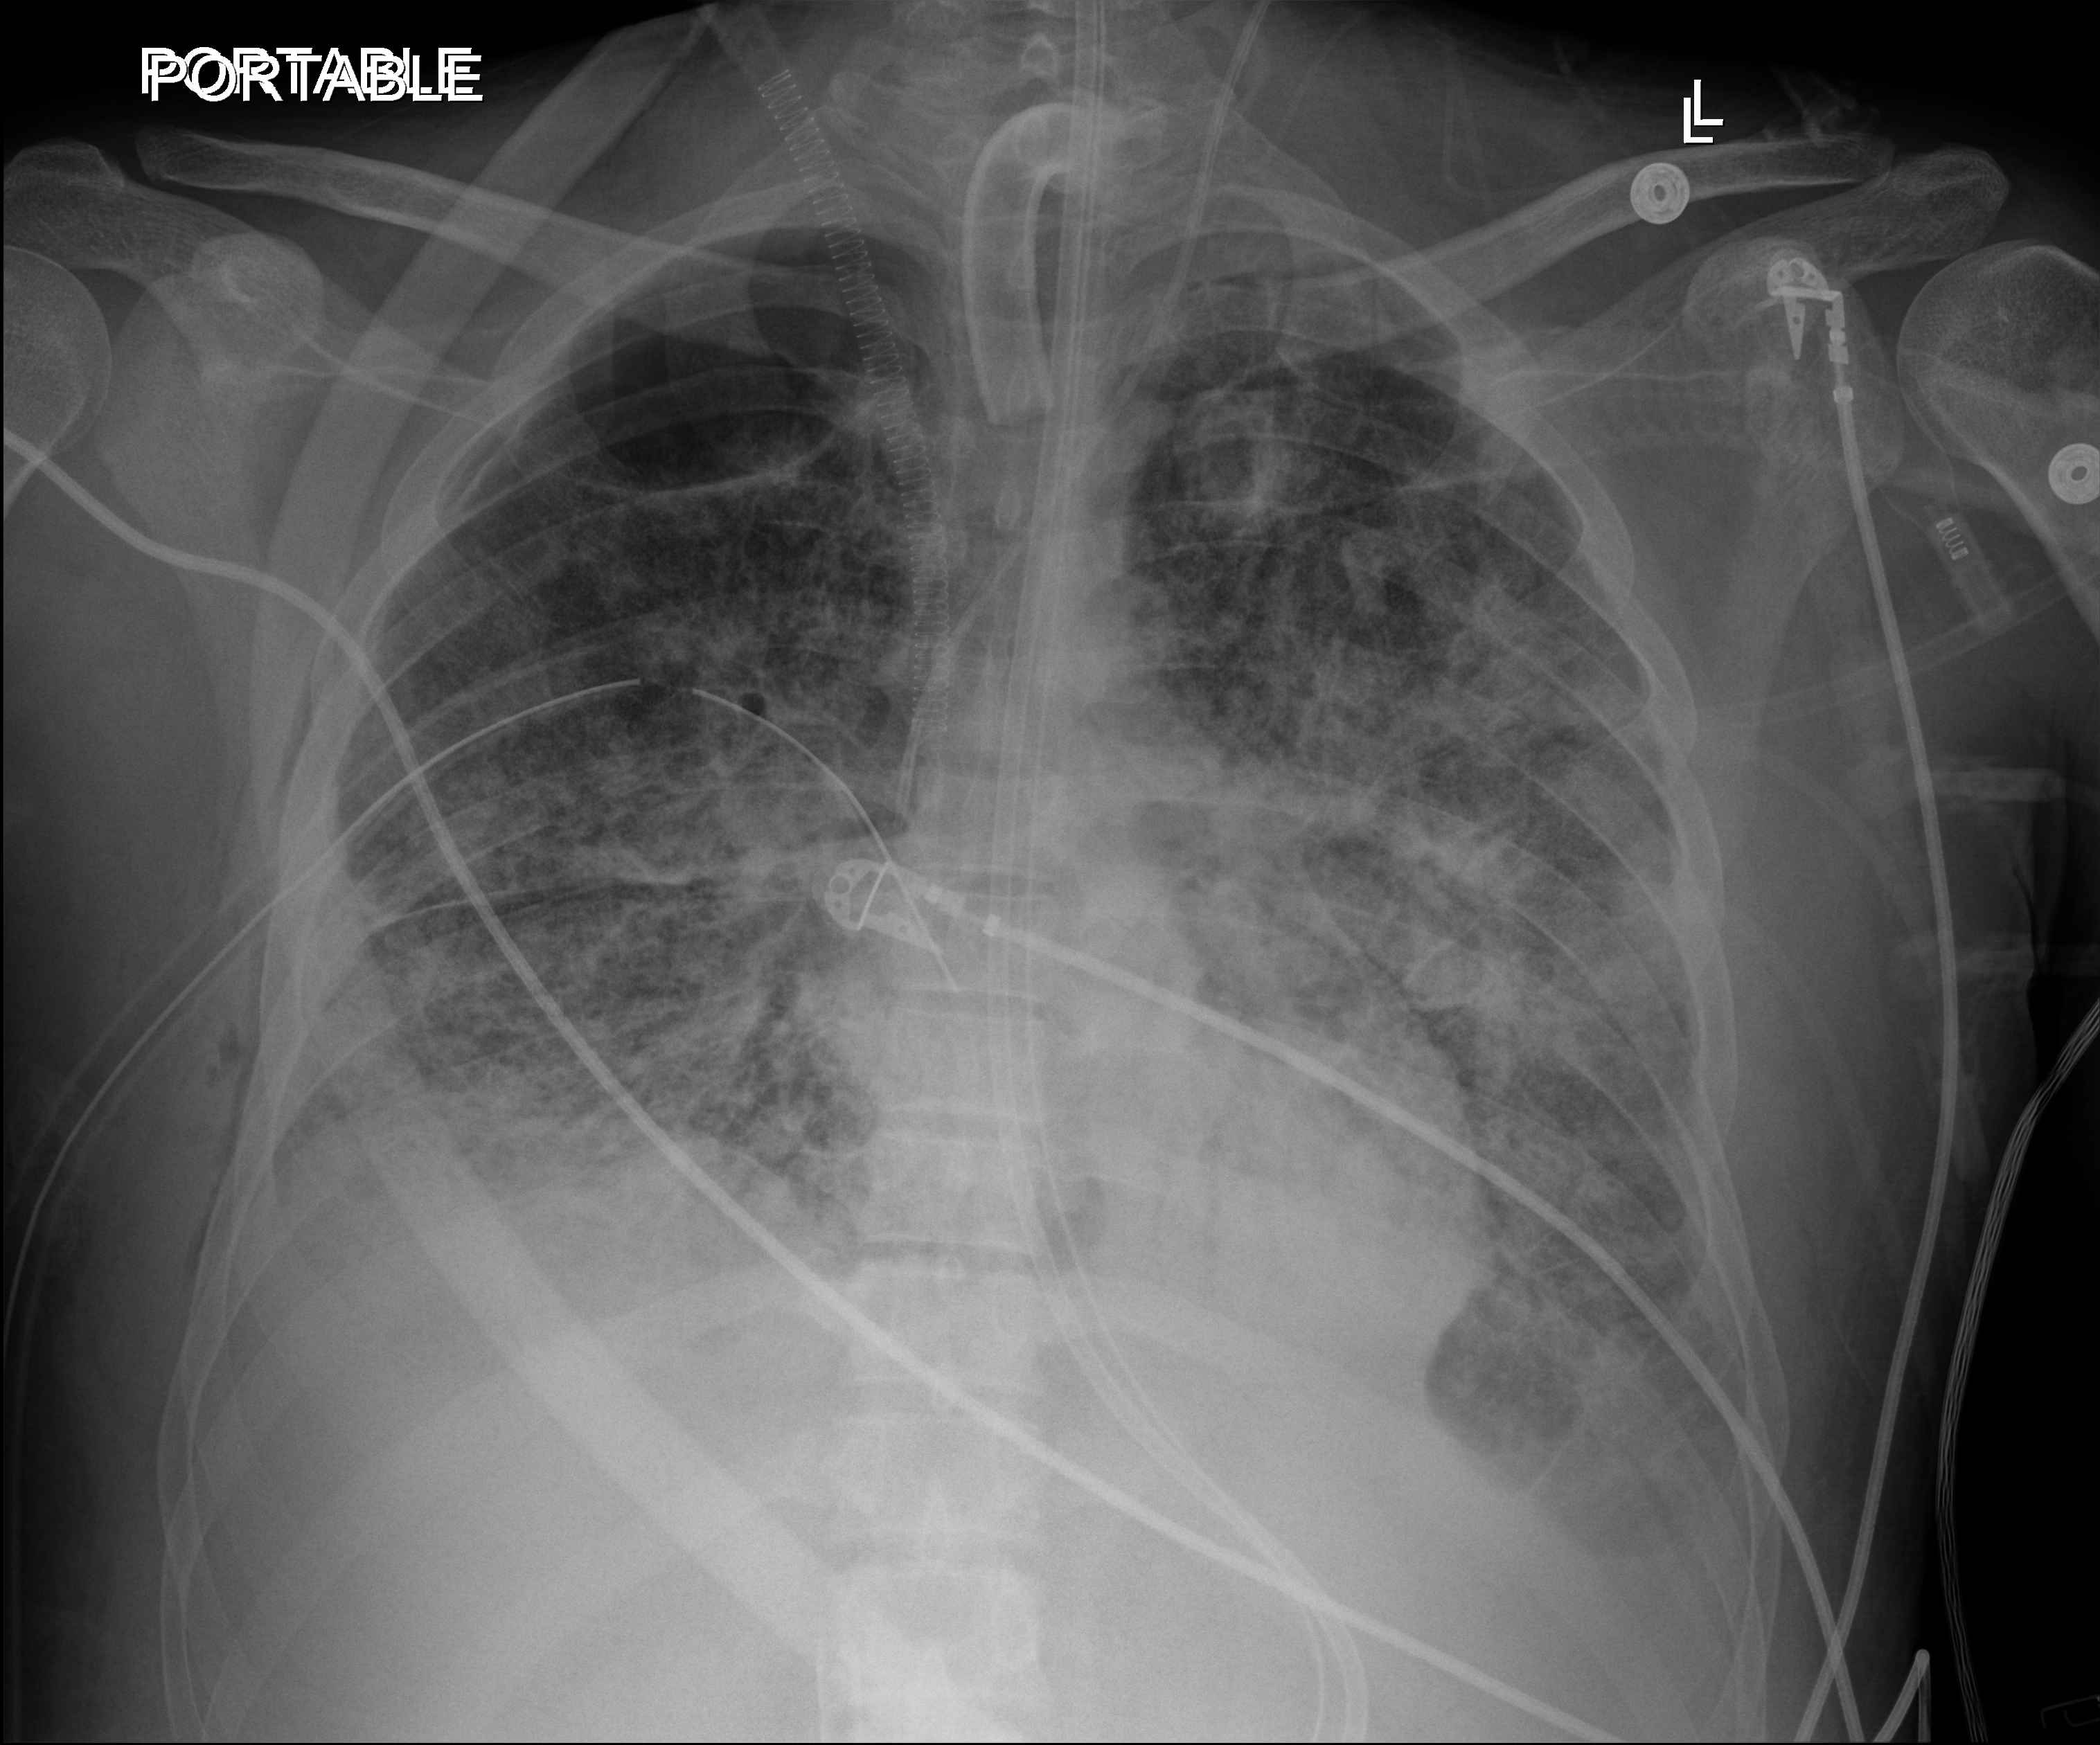
Chest radiograph (digital radiography). Patient hospitalised with COVID-19, aged 18–59 years.
Hospital-stay facts (about this admission, not read from this image; timing relative to this image not recorded): mechanically ventilated during this hospital stay: yes; smoking status (admission record): never; length of hospital stay: 60 days.